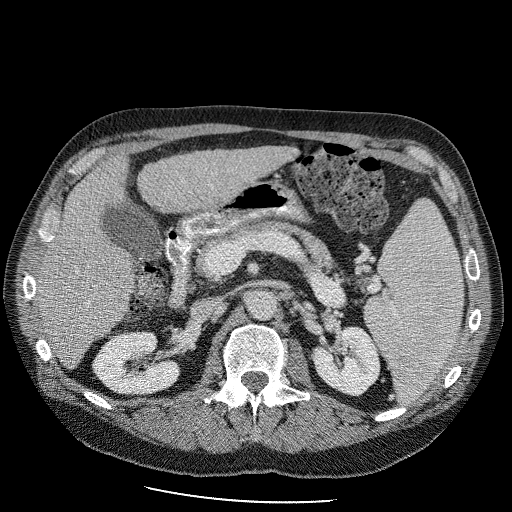
Contrast-enhanced abdominal CT (liver protocol), one axial slice; slice 43 of 98 in the series (ordered by position); soft-tissue window (W 400 / L 40 HU); 2.5 mm slice thickness; 512 × 512 image matrix. From the clinical record (not read from this slice): diagnosis: hepatocellular carcinoma (patient treated with transarterial chemoembolisation; whether this scan precedes or follows treatment is not stated here); TNM stage (as recorded): Stage-II; Child-Pugh class: B; tumour differentiation: moderately differentiated; tumour nodularity: uninodular.
Structures marked on this image (semi-automatically segmented with operator editing):
- liver parenchyma outside the tumour (the mass and vessels are separate outlines, so this box may not span the whole liver): box from (x=34, y=146) to (x=298, y=366) px
- liver vessels: (x=46, y=234)–(x=53, y=240)